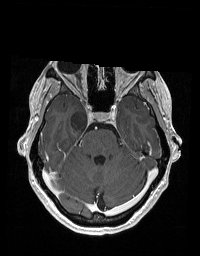
Brain MRI from a brain-tumour surgery series, one axial slice. Slice 127 of 192 in the series (ordered by position). T1-weighted post-contrast. 1 mm slice thickness. 200 × 256 image matrix, field of view 195 × 250 mm. From the clinical record (not read from this slice): histopathology: Glioblastoma; WHO grade: 2; IDH mutation: no; tumour location: Right Skull Base Temporal.
Structures marked on this image (outlined manually by an expert reader):
- tumour: bounding box [x1, y1, x2, y2] px = [71, 110, 98, 132]